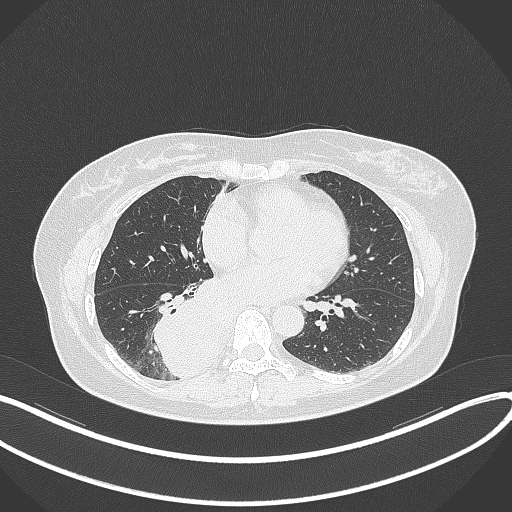
Chest CT, one axial slice; slice 153 of 331 in the series (ordered by position); reconstruction kernel B70f; lung window (W 1500 / L -600 HU); 512 × 512 image matrix, field of view 400 × 400 mm. Patient: female, 54 years. Case-level facts recorded for this patient, not image findings: clinical TNM (as recorded): T4 N0 M0.
Annotated regions visible in this slice (rectangle marked by the reading radiologist):
- lung tumour (recorded histology: adenocarcinoma): box from (x=156, y=282) to (x=243, y=380) px